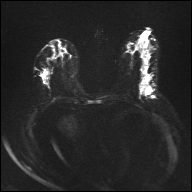
Breast MRI, one axial slice. Slice 13 of 32 in the series (ordered by position). Diffusion-weighted series; image 2 of 4 stored at this slice position (different b-values; order by instance number). 1.5 T. 192 × 192 image matrix, field of view 360 × 360 mm. Female patient.
Annotated regions visible in this slice (manually delineated by an expert):
- tumour on diffusion-weighted imaging: box from (x=145, y=82) to (x=150, y=87) px